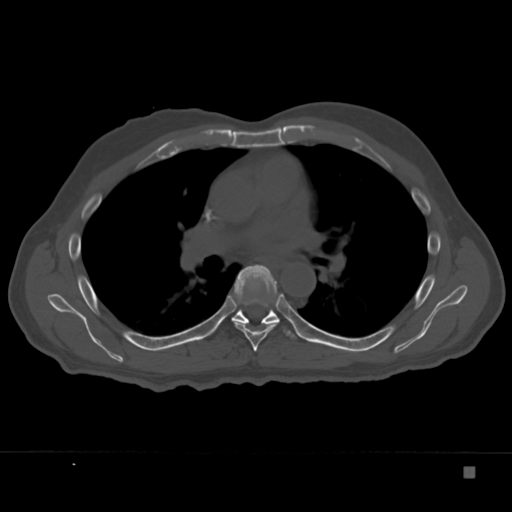
CT including the spine, one axial slice; position 233 of 332 along the scan axis; reconstruction kernel Br40s; 120 kVp; bone window (W 1800 / L 400 HU); 1.5 mm slice thickness; 512 × 512 image matrix, field of view 389 × 389 mm. Patient: male, 72 years. Case-level facts recorded for this patient, not image findings: primary cancer: skeletal.
Structures marked on this image (semi-automatically segmented with operator editing):
- T6 vertebra: bounding box <232,265,283,352> (left, top, right, bottom; pixels)
- T7 vertebra: <231,296,300,338>